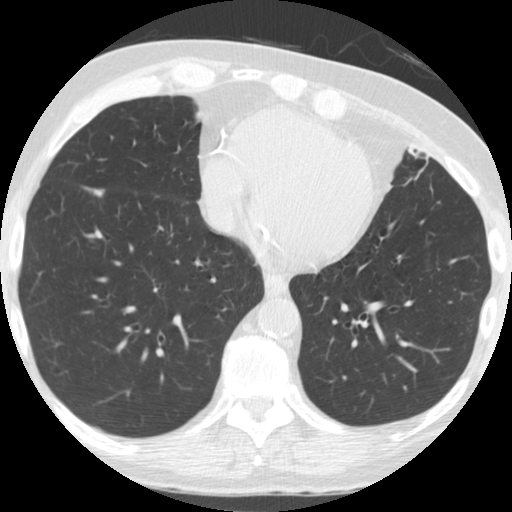
Low-dose screening chest CT, one axial slice. Slice 72 of 182 in the series (ordered by position). Reconstruction kernel STANDARD. 120 kVp. Lung window (W 1500 / L -600 HU). 2.5 mm slice thickness. 512 × 512 image matrix, field of view 320 × 320 mm.
Structures marked on this image (outlined manually by an expert reader):
- lesion 1 (tumor, lower lobe of right lung): bounding box [x1, y1, x2, y2] px = [85, 188, 104, 197]